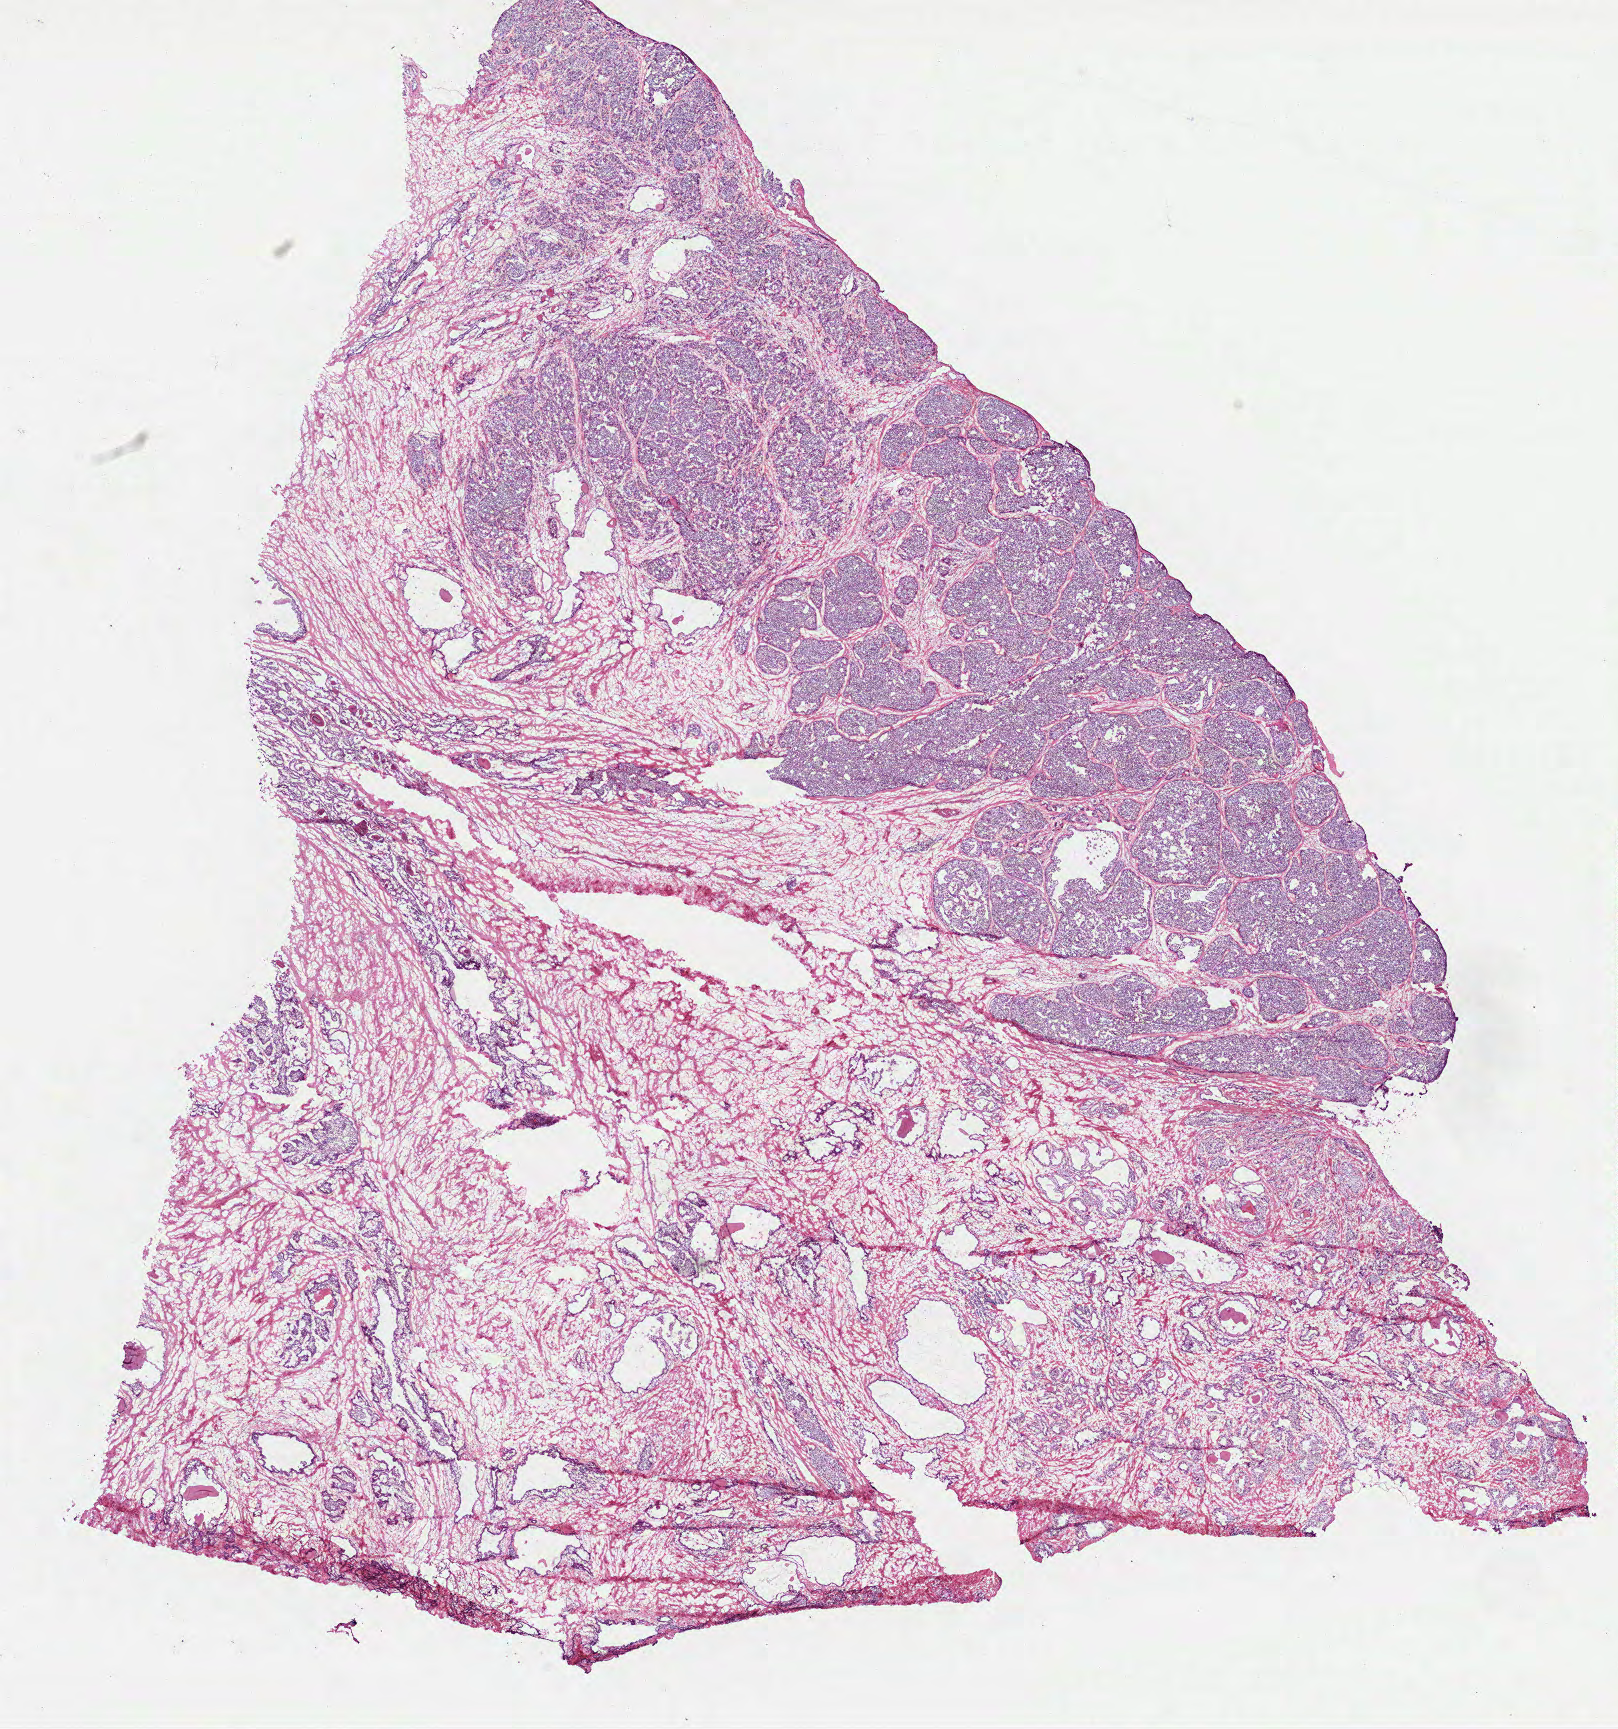
Digitized H&E-stained tissue section (whole slide) — a low-resolution overview of the entire scanned area, about 13.1 x 13.9 mm (slide scanned at 40x). Frozen section from the top of the tissue portion. Primary tumour sample from the prostate. Male patient; age at initial diagnosis 70 years. Gleason score: 7 (4+3). Pathologist review of this section (percent, as recorded): tumour cells 40%, tumour nuclei 60%, normal cells 30%, stromal cells 30%, necrosis 0%. Inflammatory infiltration, as recorded: lymphocyte infiltration 0%, monocyte infiltration 0%, neutrophil infiltration 0%.
- pathologic diagnosis: Acinar cell carcinoma (prostate gland)
- lymph nodes positive (case pathology): 0 of 17 examined
- laterality: bilateral